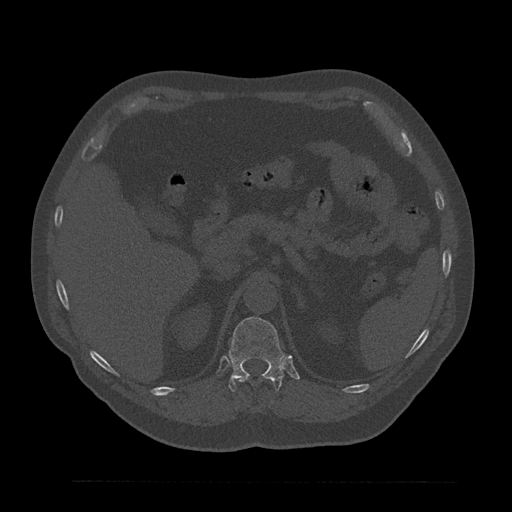
CT including the spine, one axial slice; slice 247 of 797 in the series (ordered by position); 120 kVp; bone window (W 1800 / L 400 HU); 0.5 mm slice thickness; 512 × 512 image matrix, field of view 430 × 430 mm. Patient: male, 61 years. From the clinical record (not read from this slice): primary cancer: prostate.
Structures marked on this image (semi-automatic segmentation, software-assisted and operator-edited):
- T11 vertebra: bounding box <239,378,271,382> (left, top, right, bottom; pixels)
- T12 vertebra: <228,317,285,392>